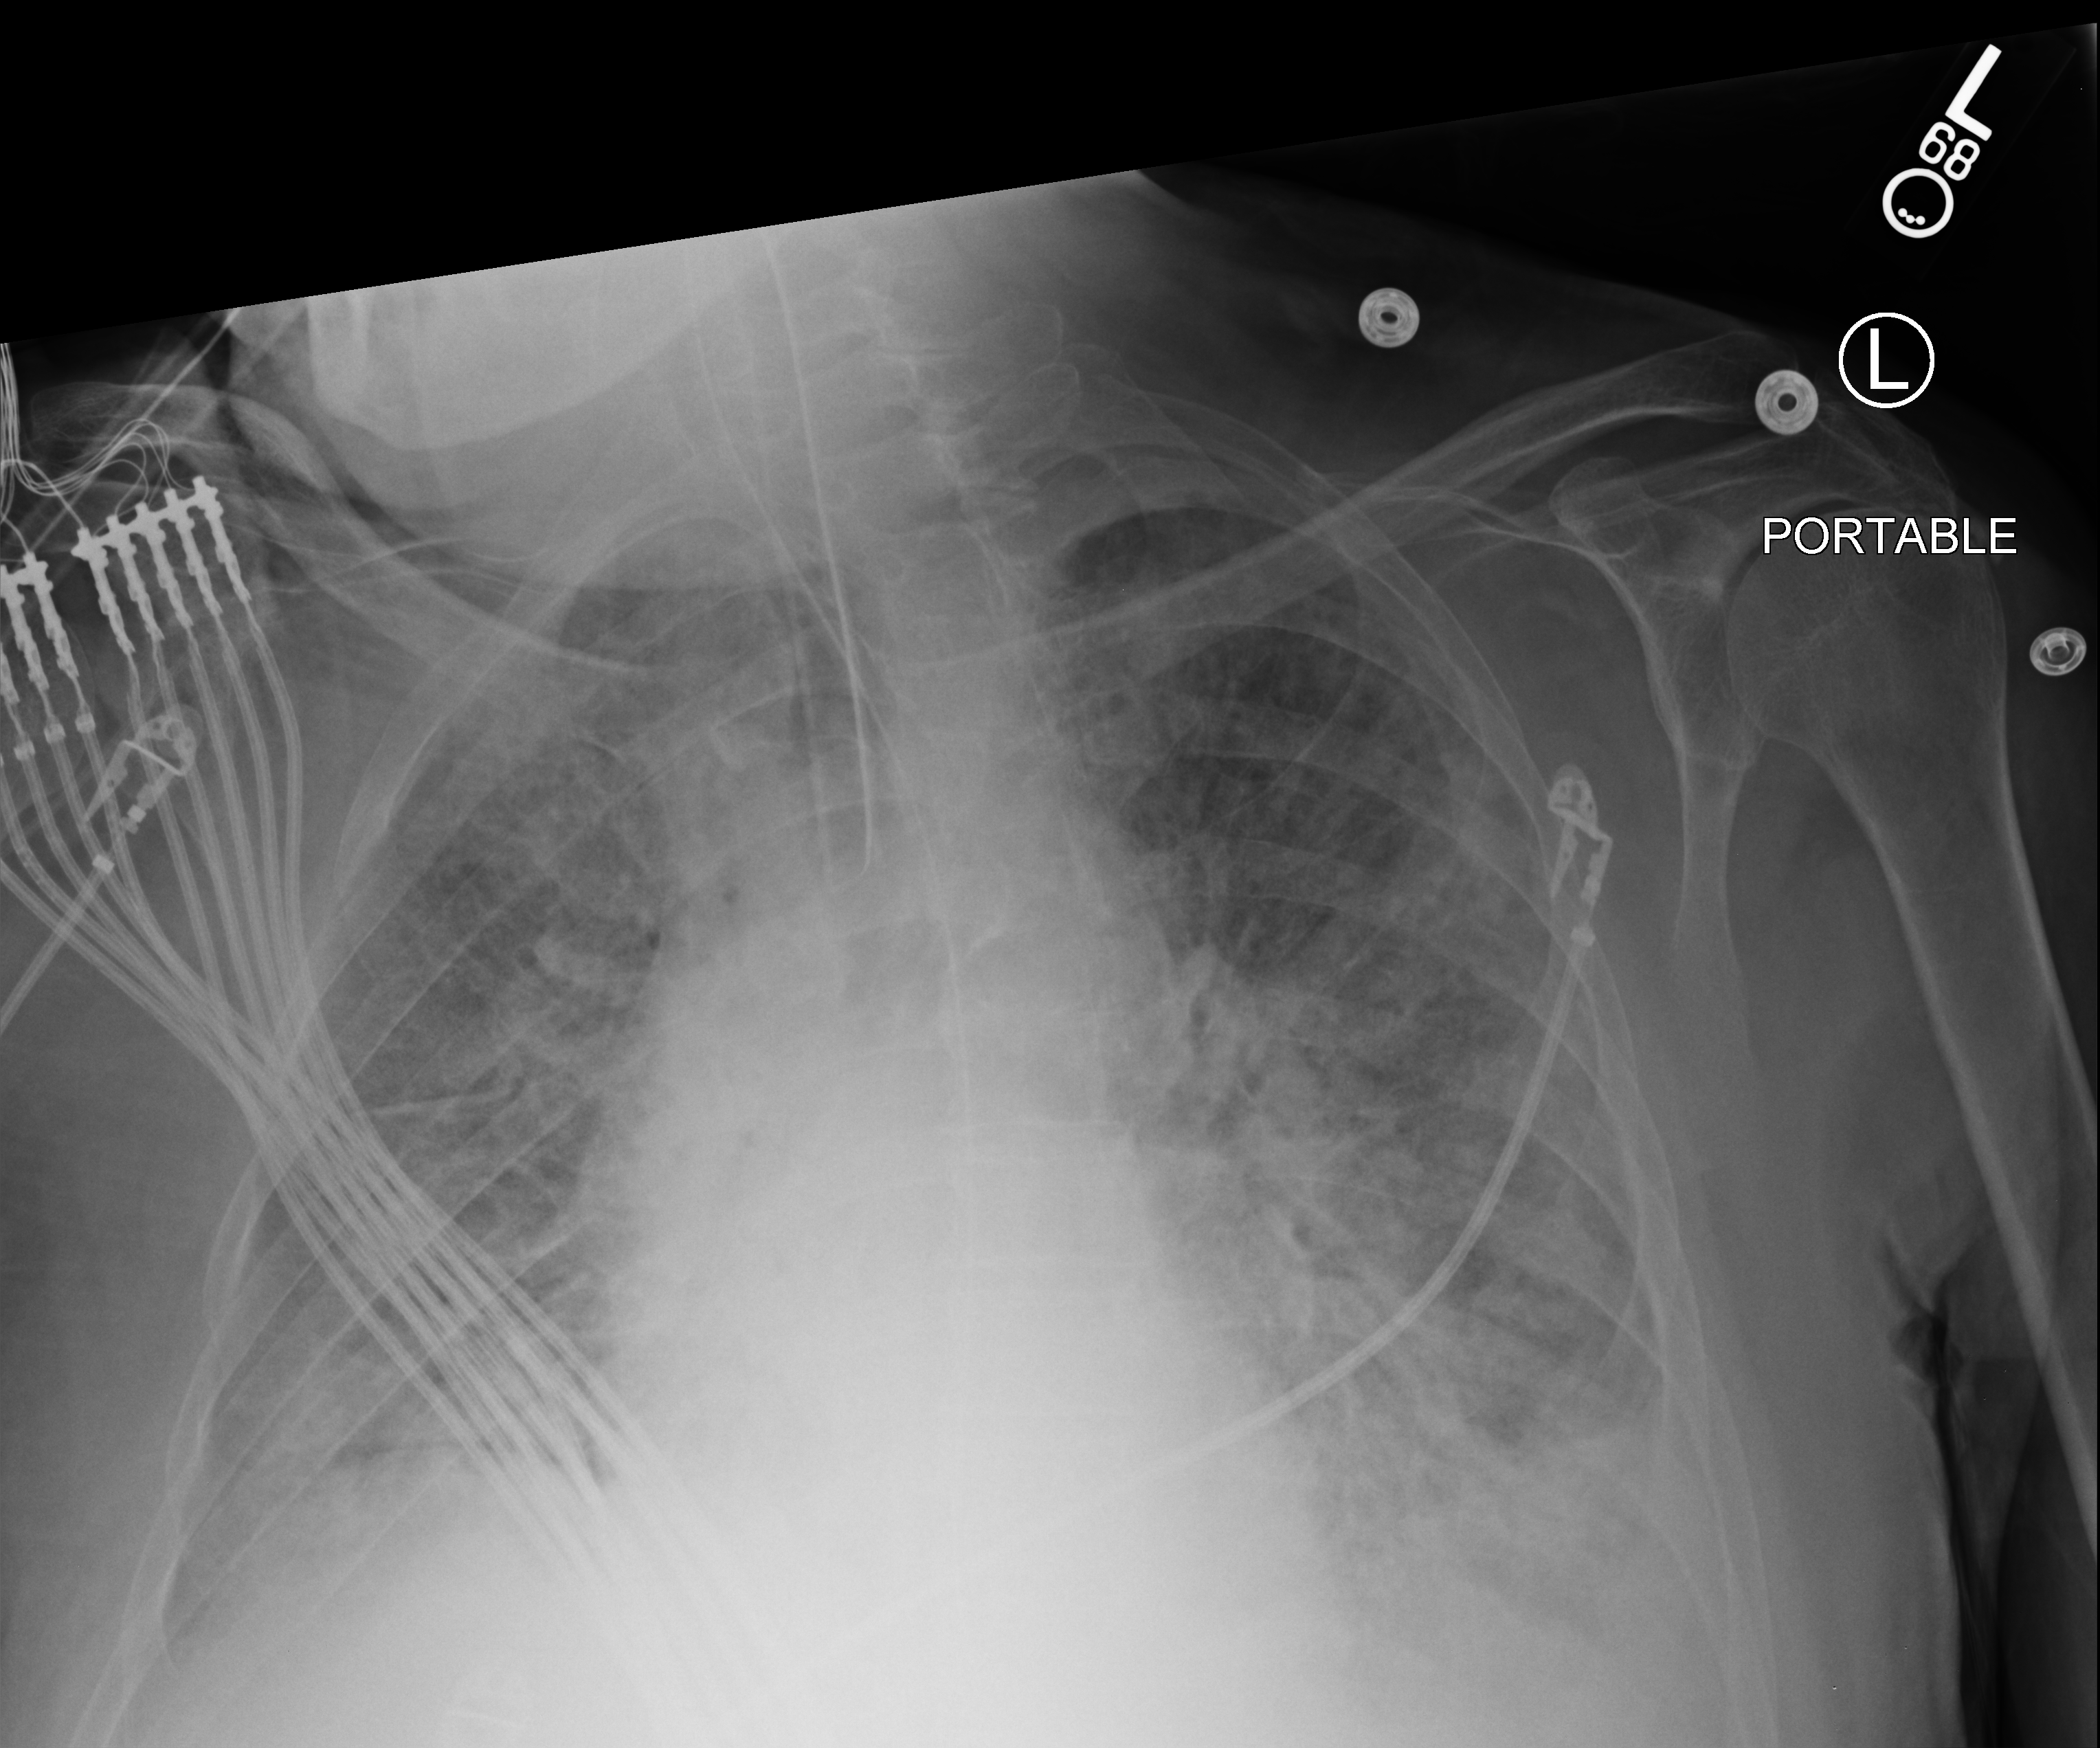
Chest X-ray (portable), anteroposterior (AP) projection. Patient hospitalised with COVID-19; male, aged 60–74 years.
Hospital-stay facts (about this admission, not read from this image; timing relative to this image not recorded): mechanically ventilated during this hospital stay: yes; COPD (admission record): no; length of hospital stay: 25 days.